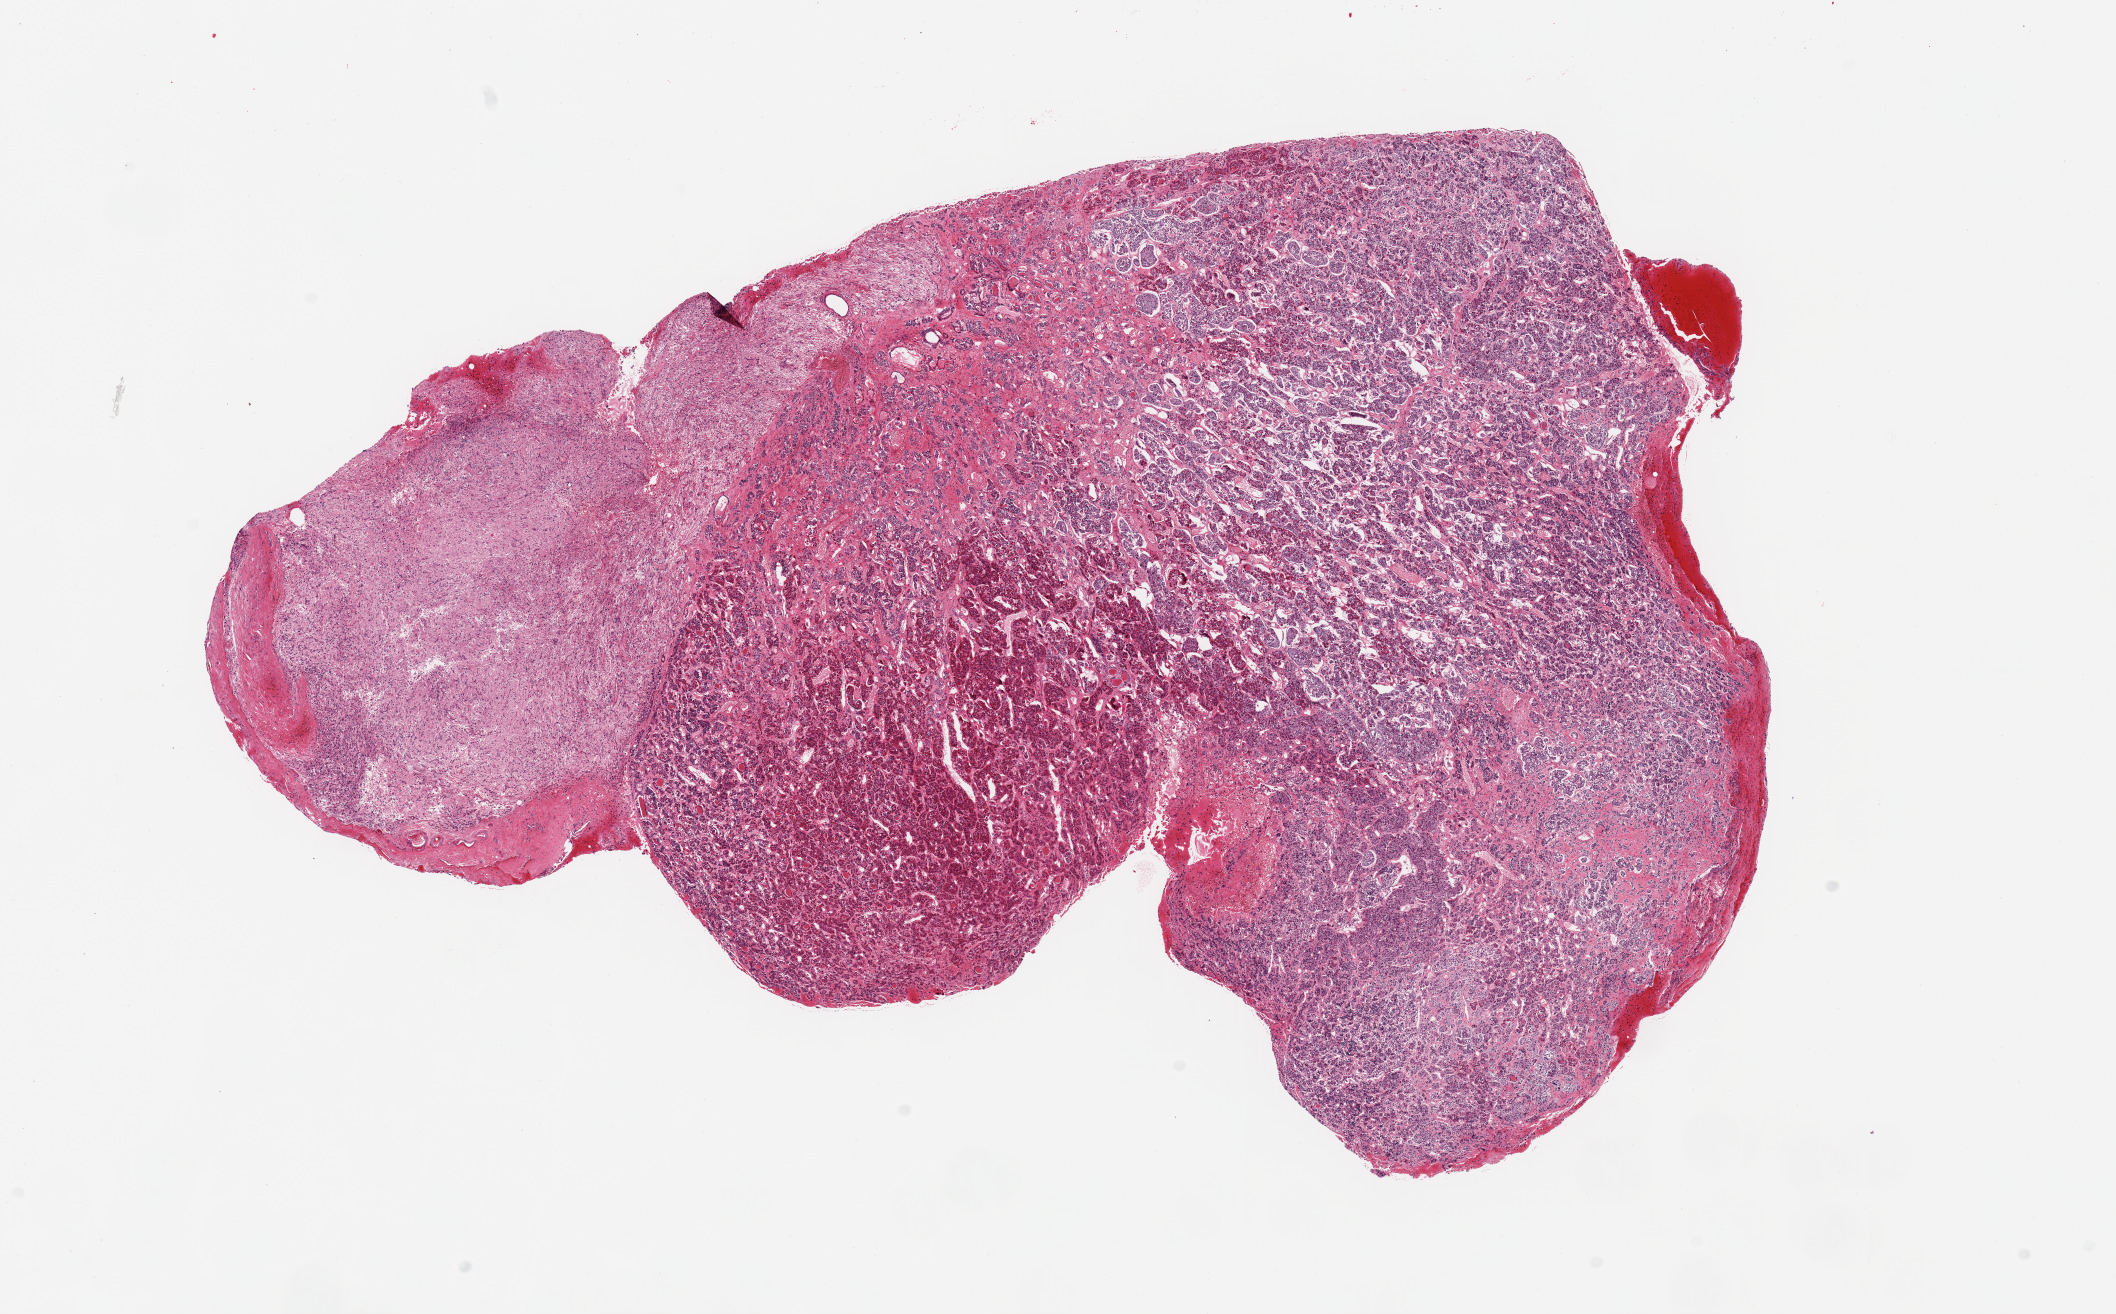
H&E whole-slide image, brightfield — a low-resolution overview of the entire scanned area, about 16.7 x 10.4 mm (acquisition: 20x scan), PAXgene-fixed, paraffin-embedded tissue, sampled site (target tissue): pituitary, donor tissue sample. Female donor.
* review note (as recorded): 1 piece; autolysis varies from 1 to 2 in anterior lobe; posterior lobe = 1